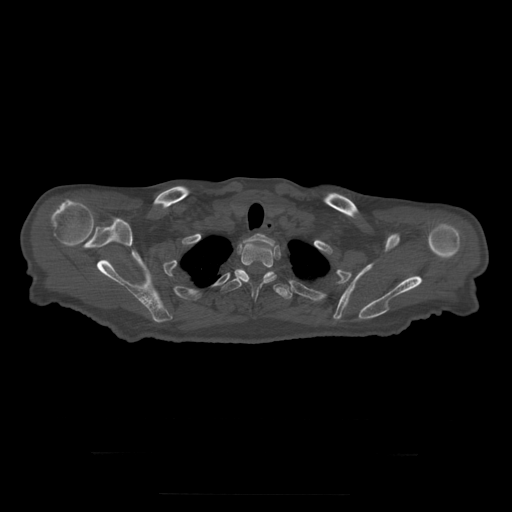
CT including the spine, one axial slice; slice 269 of 397 in the series (ordered by position); reconstruction kernel STANDARD; bone window (W 1800 / L 400 HU); 1.25 mm slice thickness; 512 × 512 image matrix. Patient age 73 years. From the clinical record (not read from this slice): primary cancer: prostate.
Outlined on this slice (semi-automatically segmented with operator editing):
- T1 vertebra: box from (x=244, y=234) to (x=275, y=246) px
- T2 vertebra: (x=236, y=242)–(x=277, y=299)
- T3 vertebra: (x=221, y=269)–(x=293, y=299)